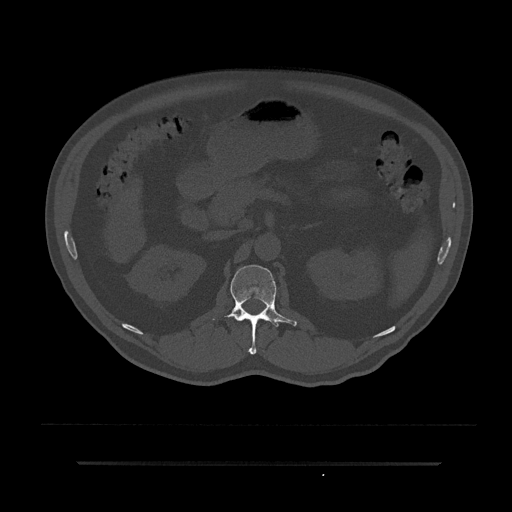
CT including the spine, one axial slice; slice 146 of 797 in the series (ordered by position); reconstruction kernel Br40s/3; 120 kVp; bone window (W 1800 / L 400 HU); 0.5 mm slice thickness; 512 × 512 image matrix, field of view 464 × 464 mm. Male patient, age 59 years. From the clinical record (not read from this slice): primary cancer: bile ducts.
Structures marked on this image (semi-automatic segmentation, software-assisted and operator-edited):
- L1 vertebra: box from (x=212, y=265) to (x=297, y=355) px